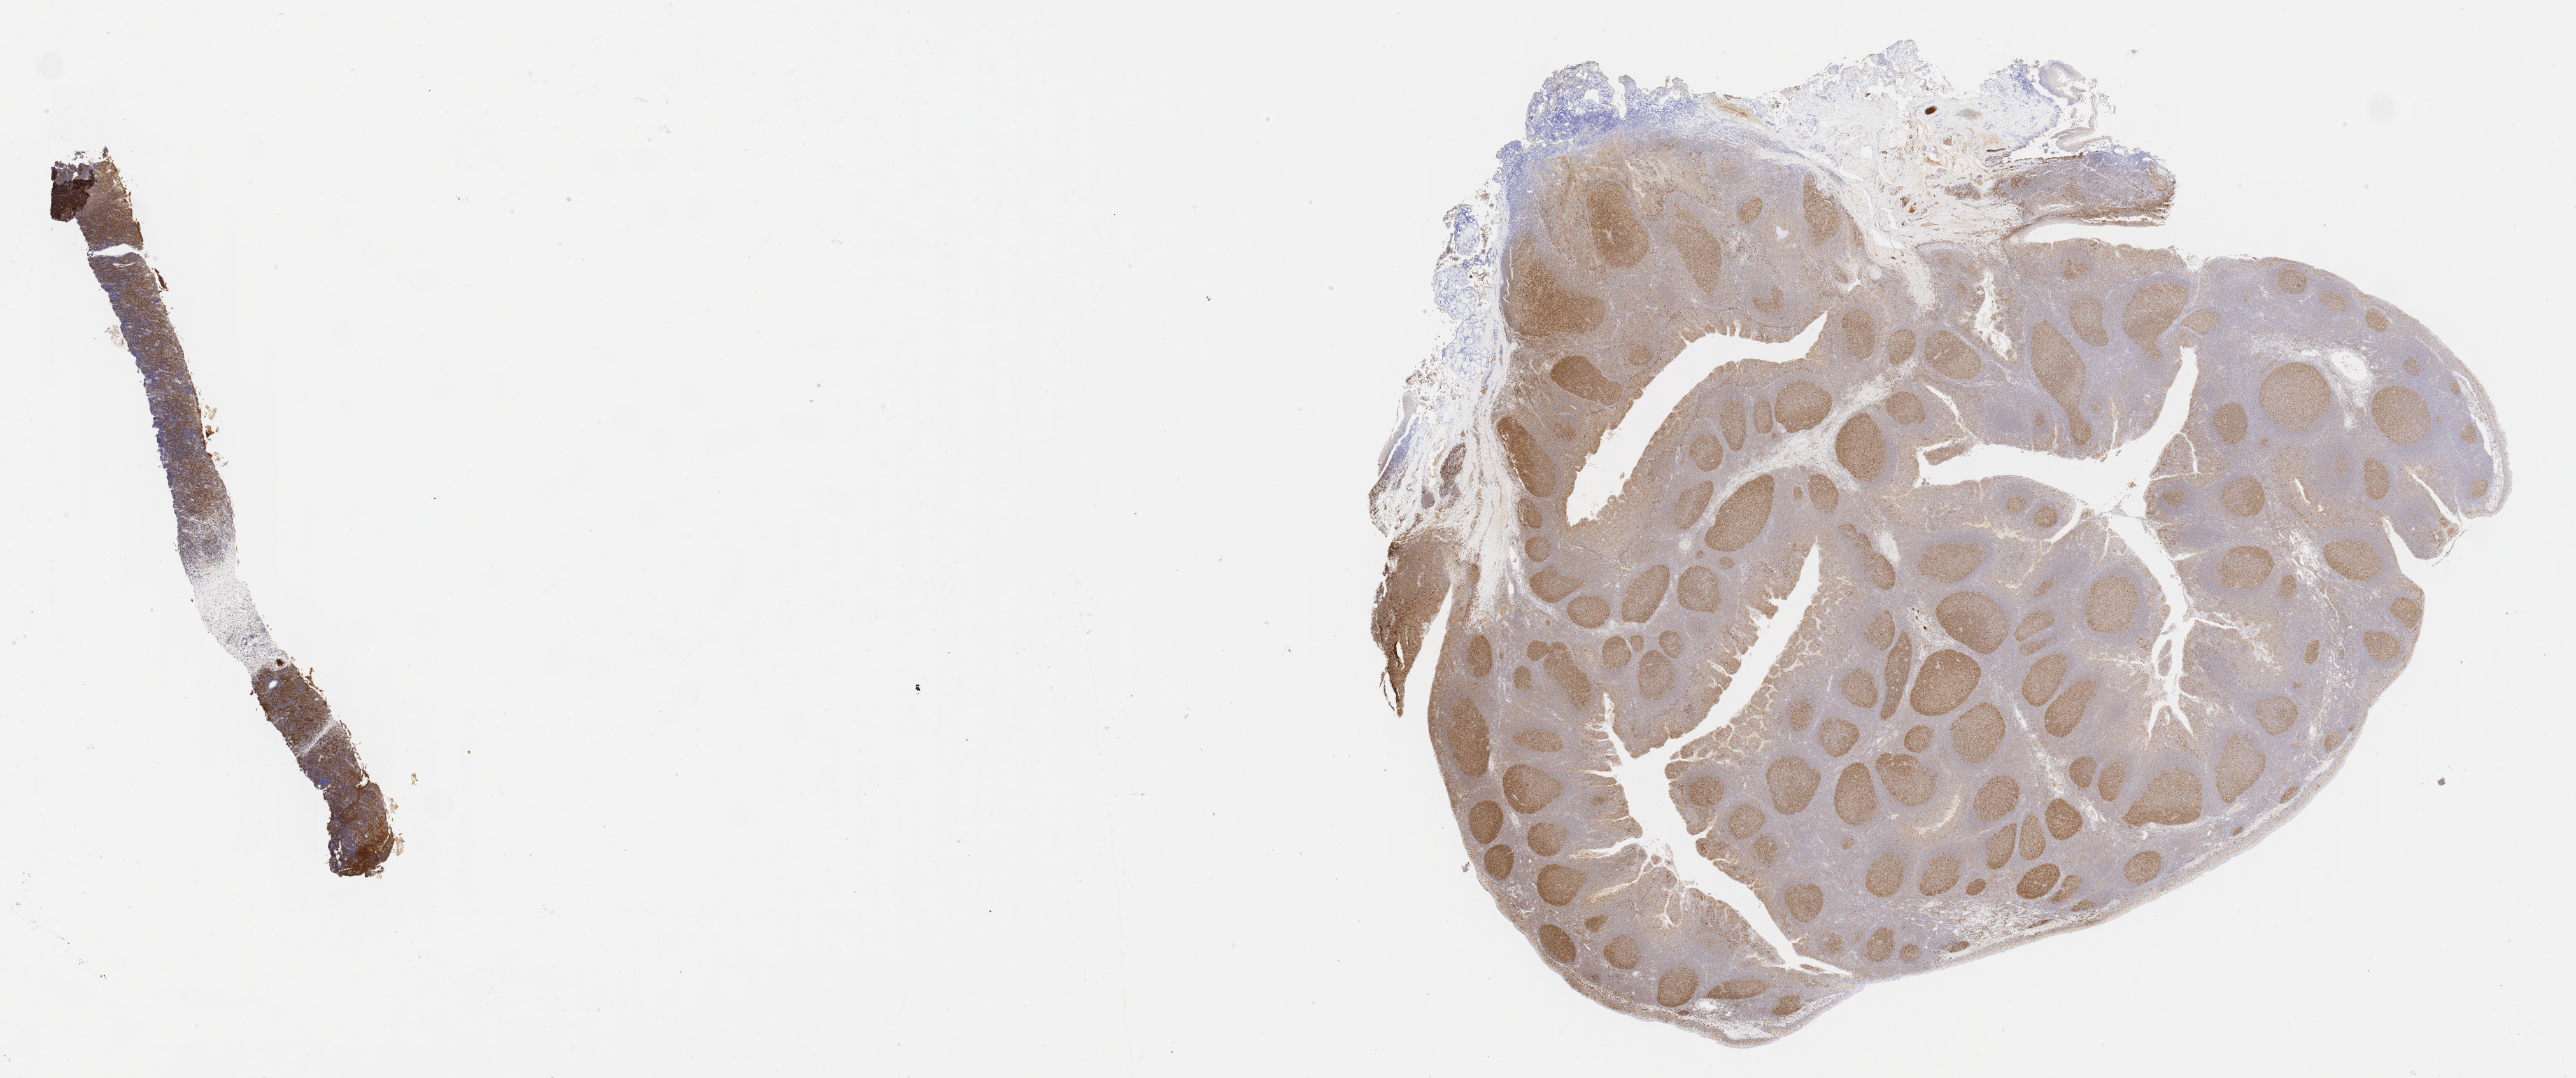
Whole-slide image, immunohistochemical stain for BCL6 — a low-resolution overview of the entire scanned area, about 32.7 x 13.7 mm; specimen: tumor tissue. Patient: male, age at initial diagnosis 7 years.
Histologic diagnosis: Neoplasm, uncertain whether benign or malignant.